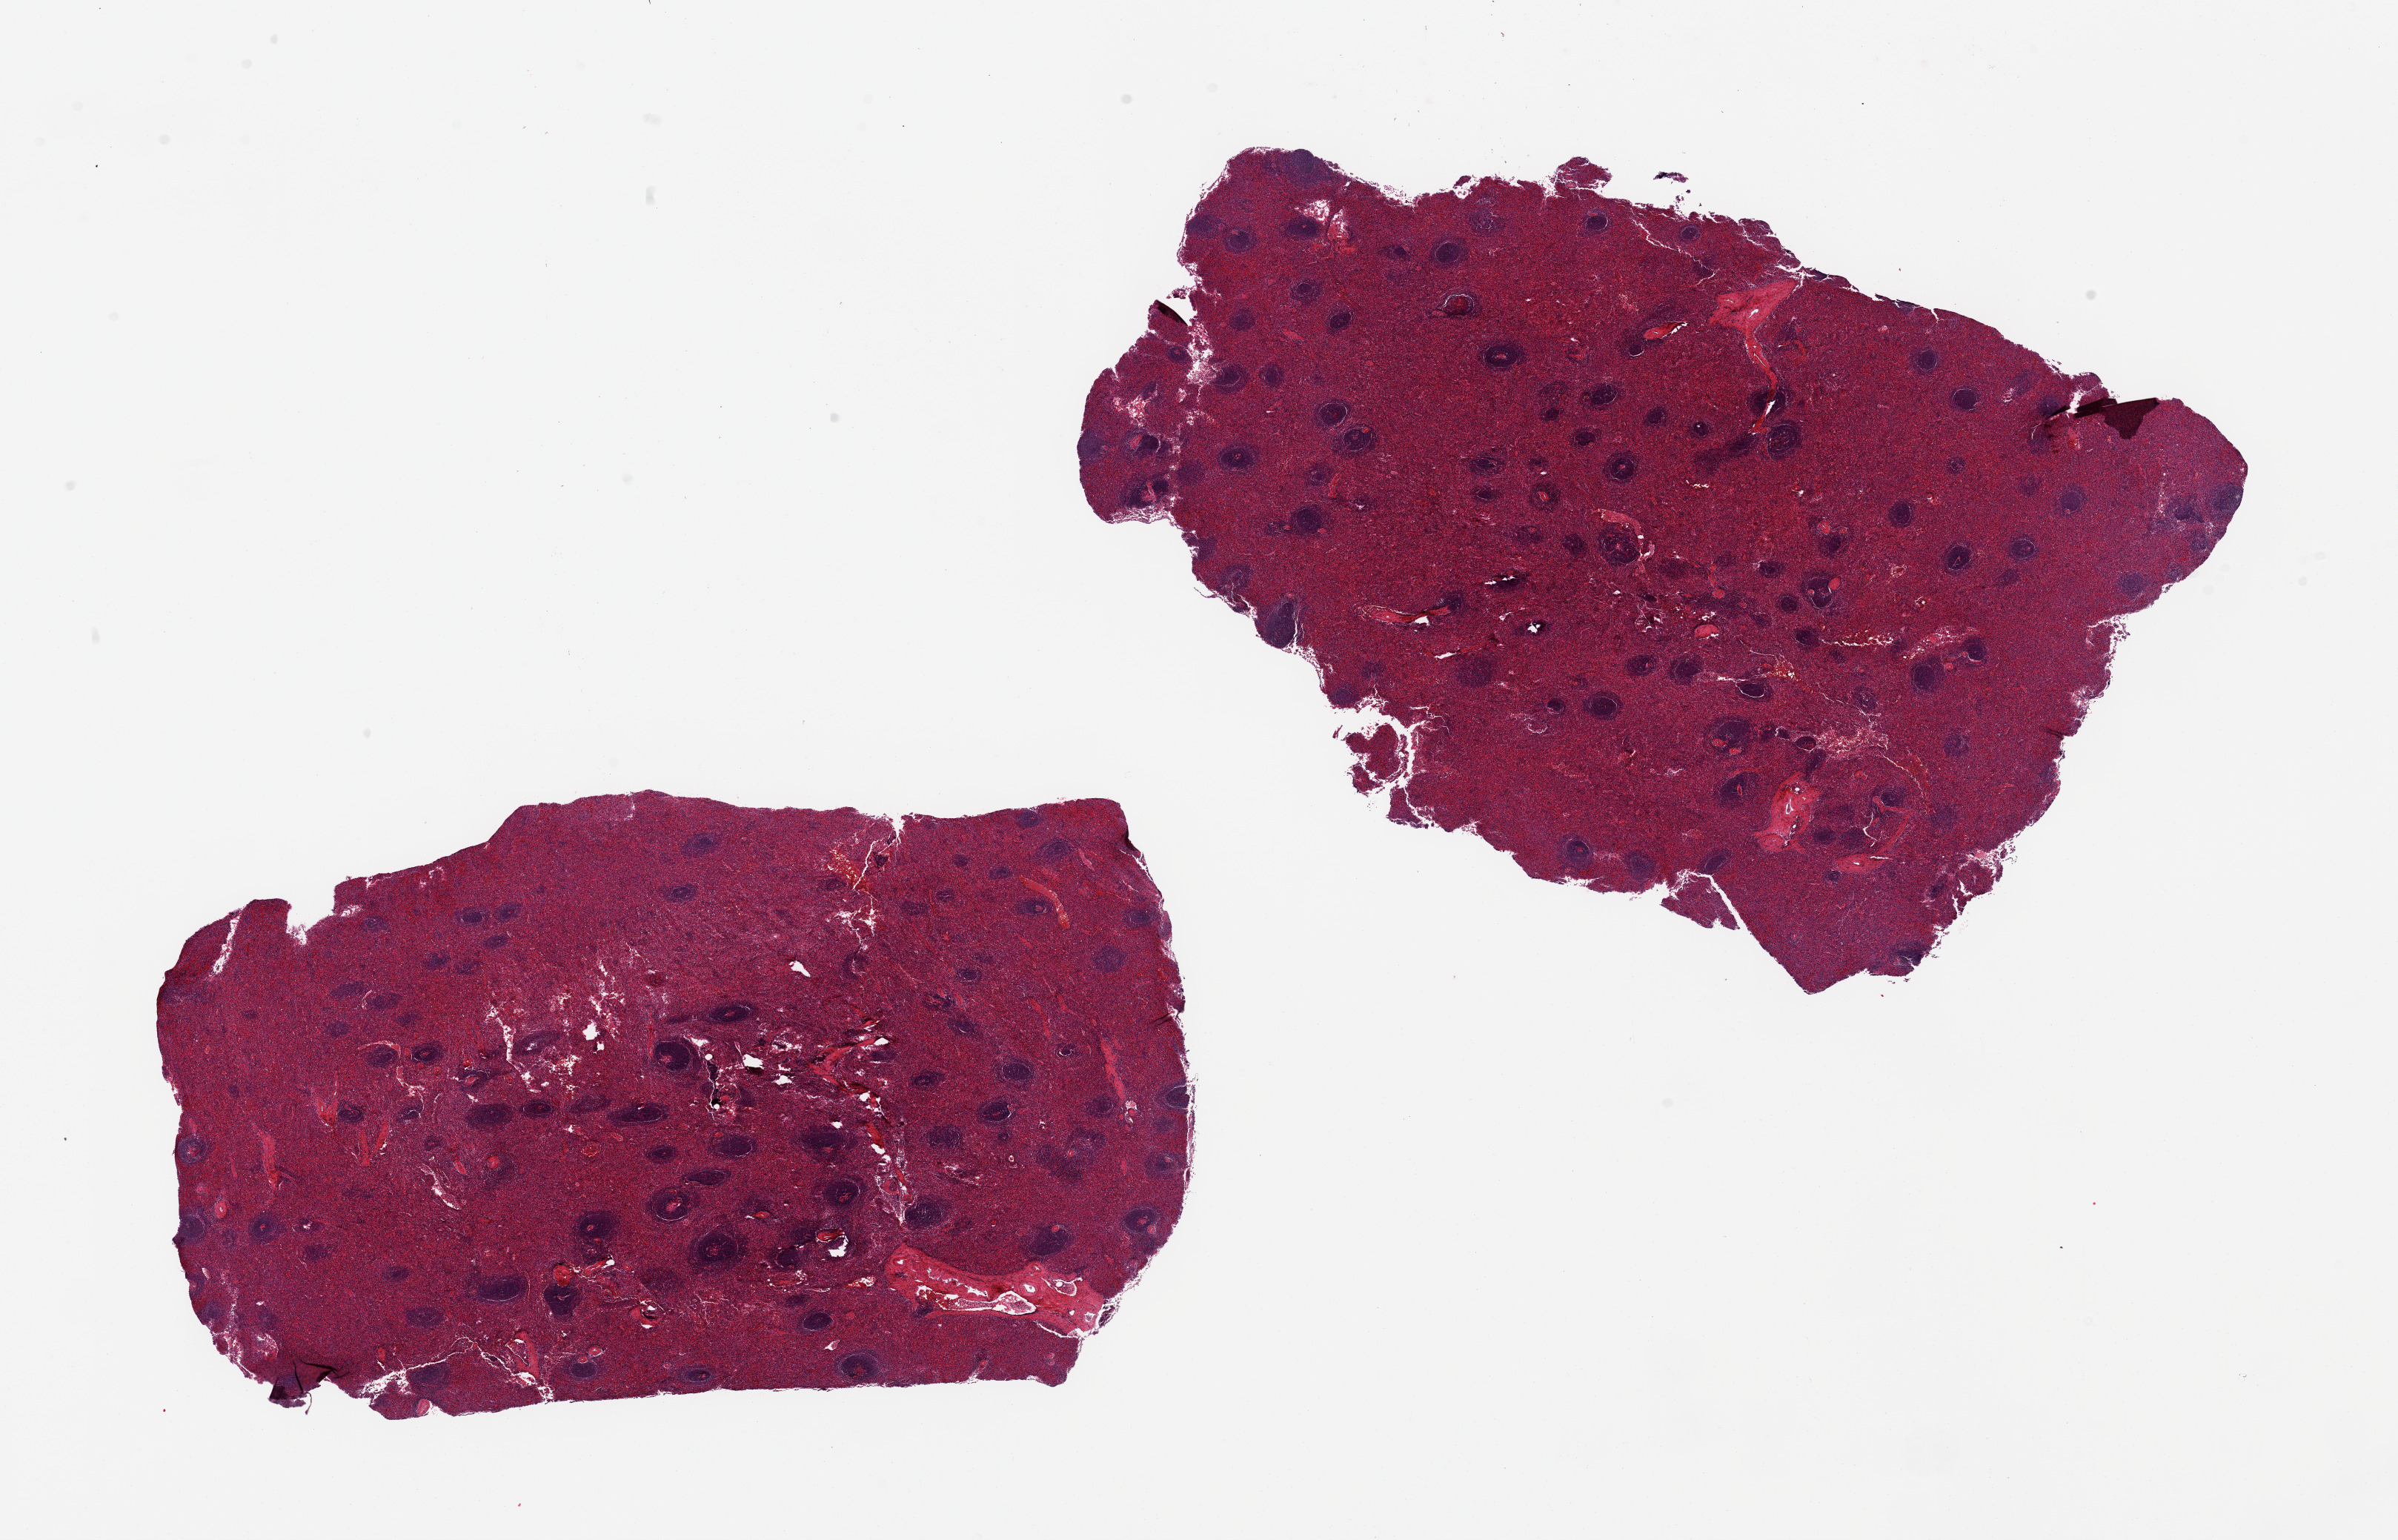
Digitized H&E-stained section — a low-resolution overview of the entire scanned area, about 25.6 x 16.4 mm (from a 20x scan); PAXgene-fixed paraffin-embedded (PFPE) section; section of spleen (target tissue); tissue donor sample. Donor sex: female.
Review note (as recorded): 2 pieces.